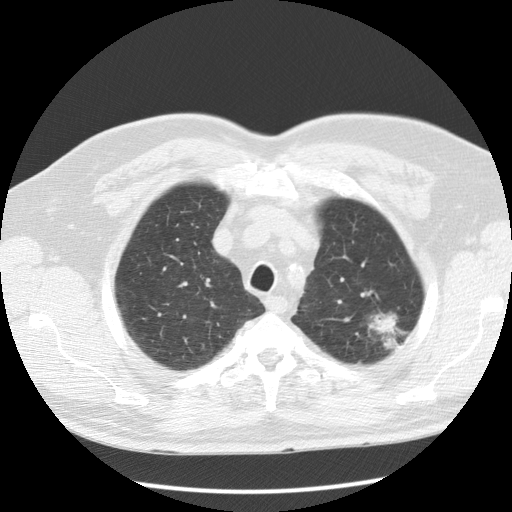
Low-dose screening chest CT, one axial slice; slice 102 of 123 in the series (ordered by position); lung window (W 1500 / L -600 HU); 2.5 mm slice thickness; 512 × 512 image matrix.
Annotated regions visible in this slice (outlined manually by an expert reader):
- lesion 1 (tumor, upper lobe of left lung): bounding box (x1, y1, x2, y2) in pixels: (372, 314, 394, 334)